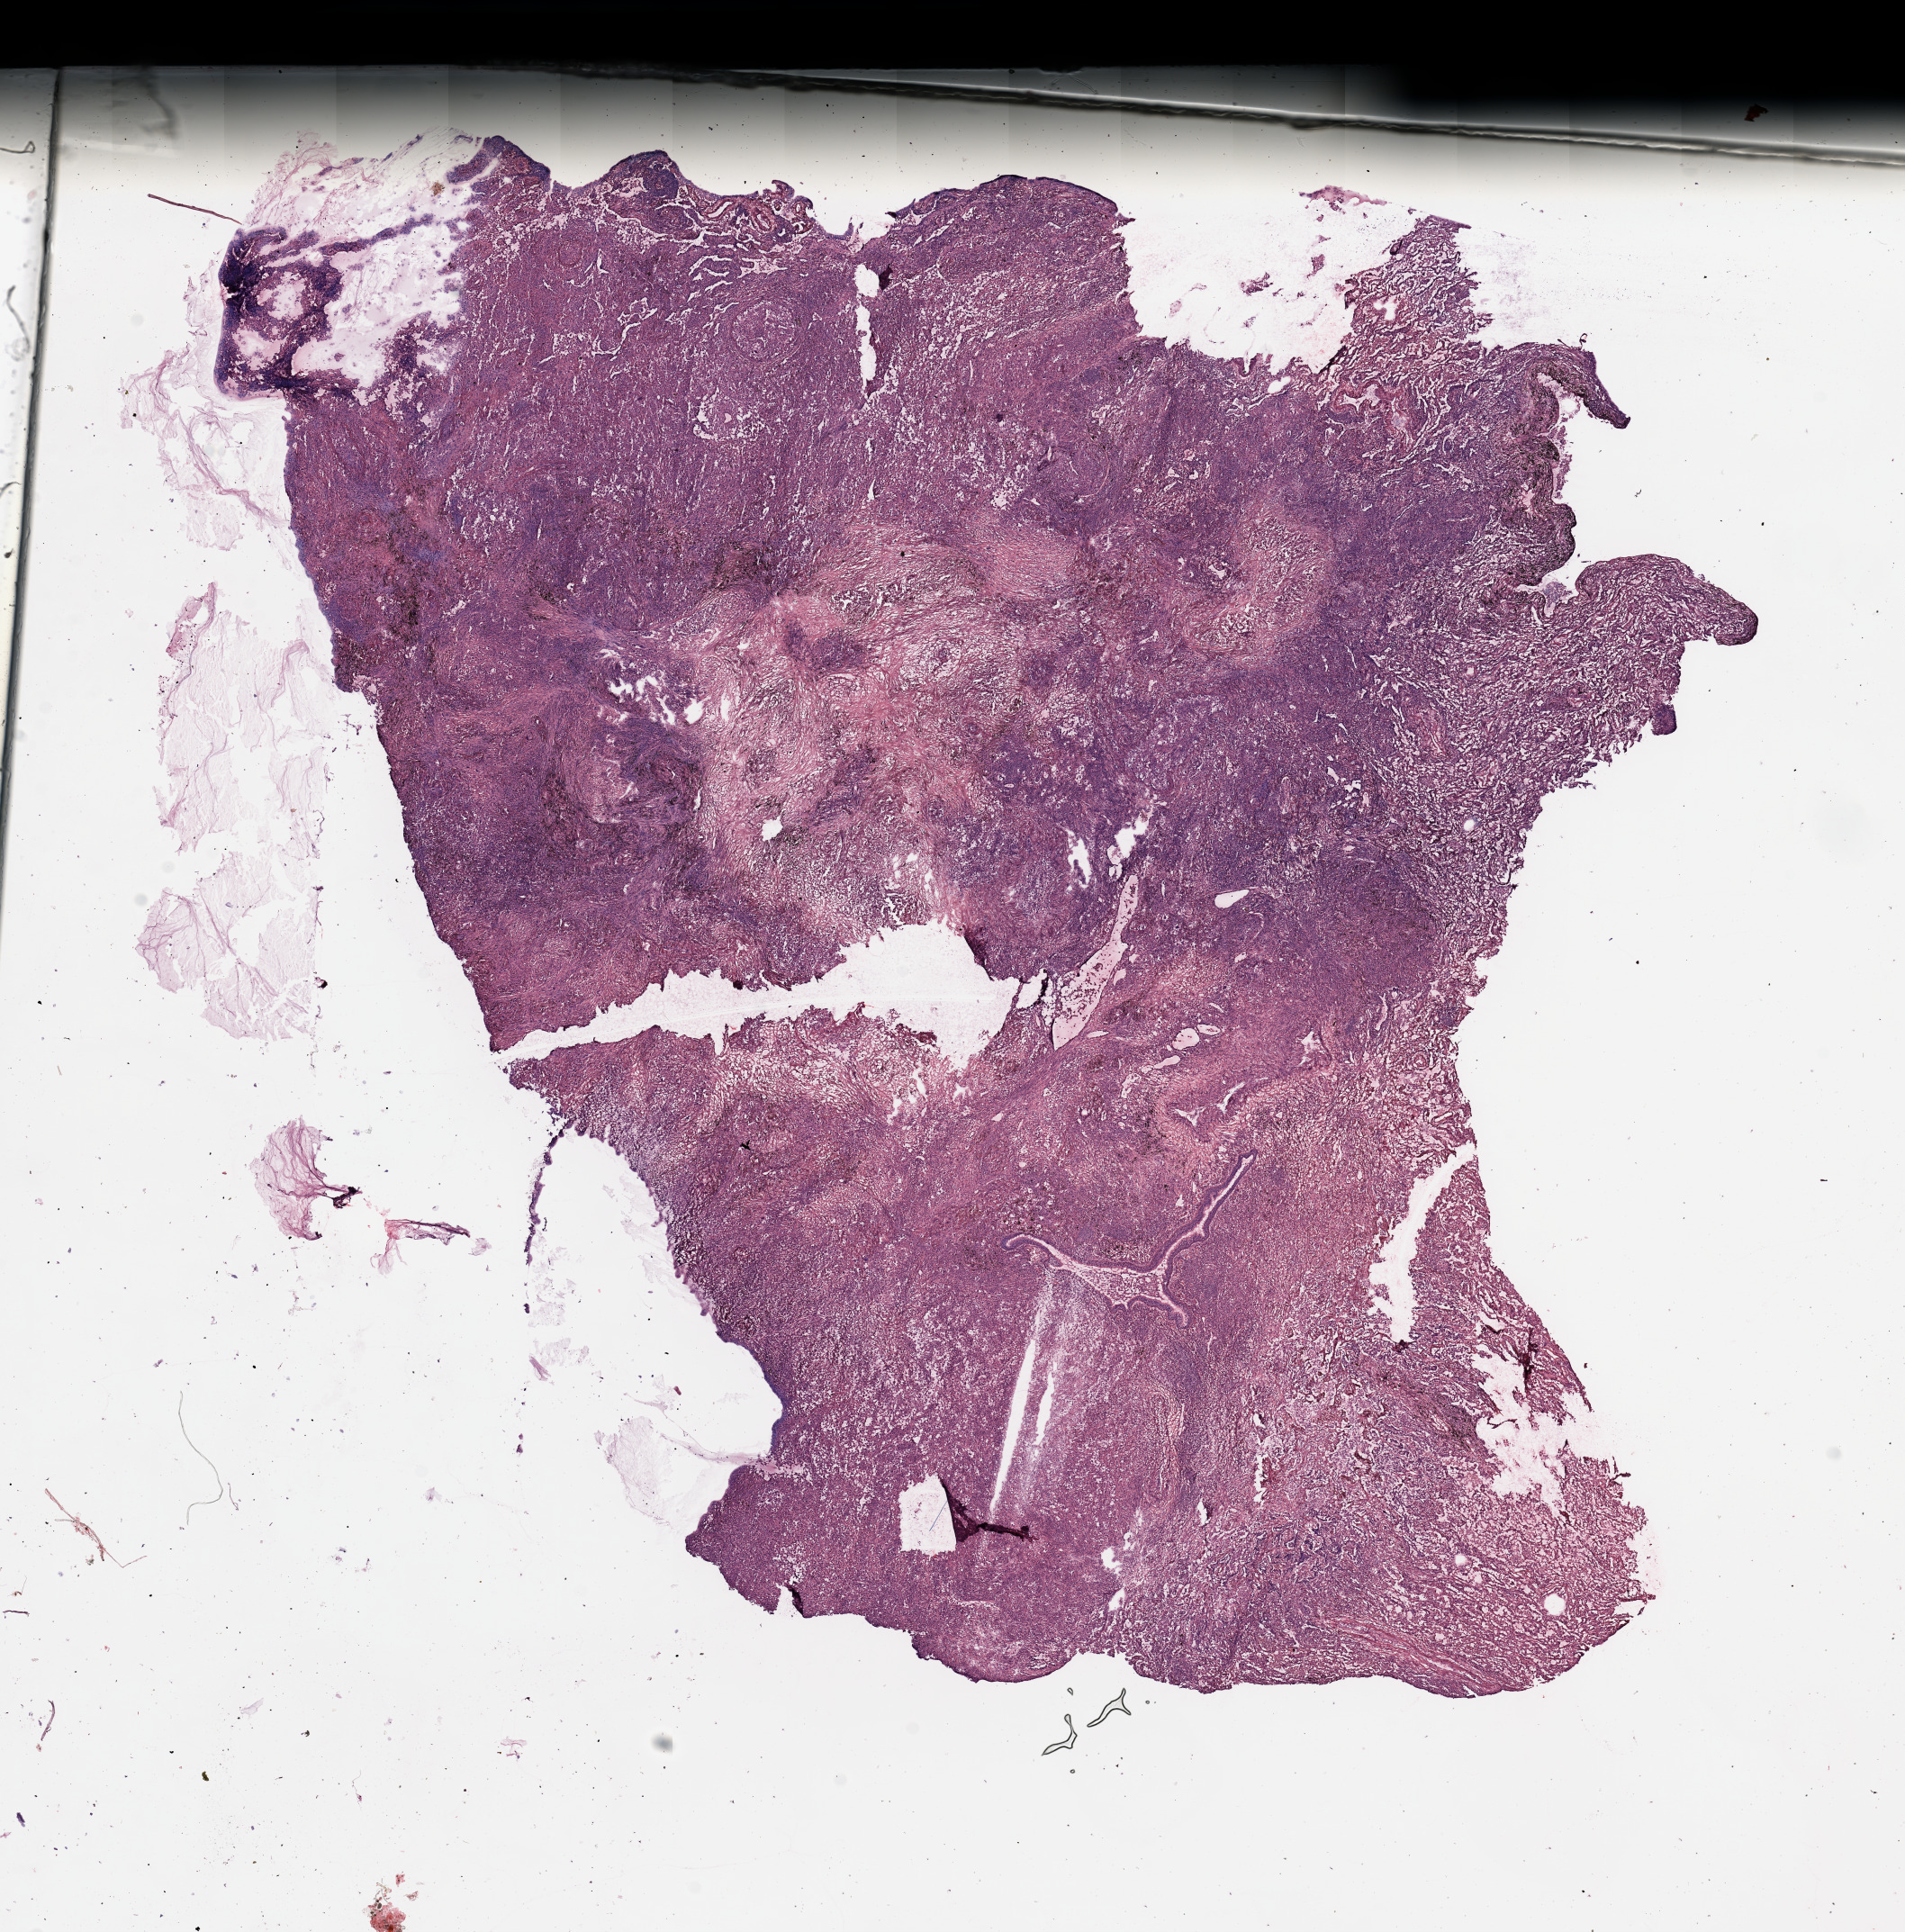
Digitized H&E-stained tissue section (whole slide), a low-resolution overview of the entire scanned area, about 16.7 x 17.0 mm, tumour tissue sample, lung. Patient: male, age 57 years.
Diagnosis: Adenocarcinoma, NOS.